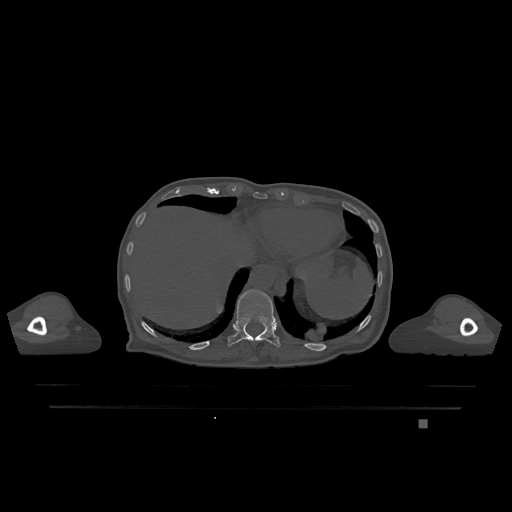
CT including the spine, one axial slice; slice 595 of 1317 in the series (ordered by position); bone window (W 1800 / L 400 HU); 512 × 512 image matrix, field of view 500 × 500 mm. Patient: female, 74 years. From the clinical record (not read from this slice): primary cancer: lung.
Outlined on this slice (semi-automatically segmented with operator editing):
- T11 vertebra: bounding box <227,289,281,347> (left, top, right, bottom; pixels)